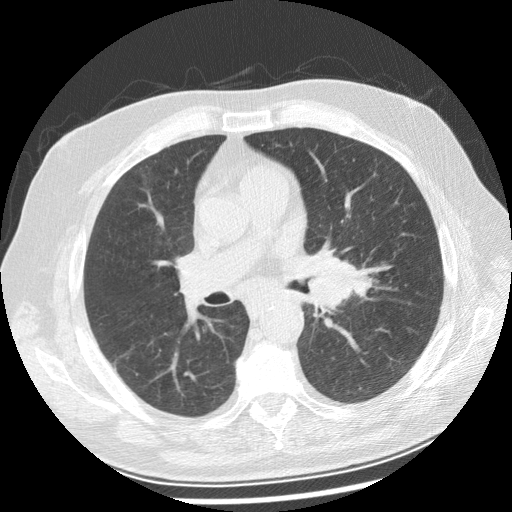
Low-dose screening chest CT, one axial slice; slice 141 of 250 in the series (ordered by position); reconstruction kernel STANDARD; 120 kVp; lung window (W 1500 / L -600 HU); 2.5 mm slice thickness; 512 × 512 image matrix, field of view 360 × 360 mm.
Annotated regions visible in this slice (manually delineated by an expert):
- lesion 1 (tumor, left main bronchus): box from (x=309, y=260) to (x=373, y=309) px